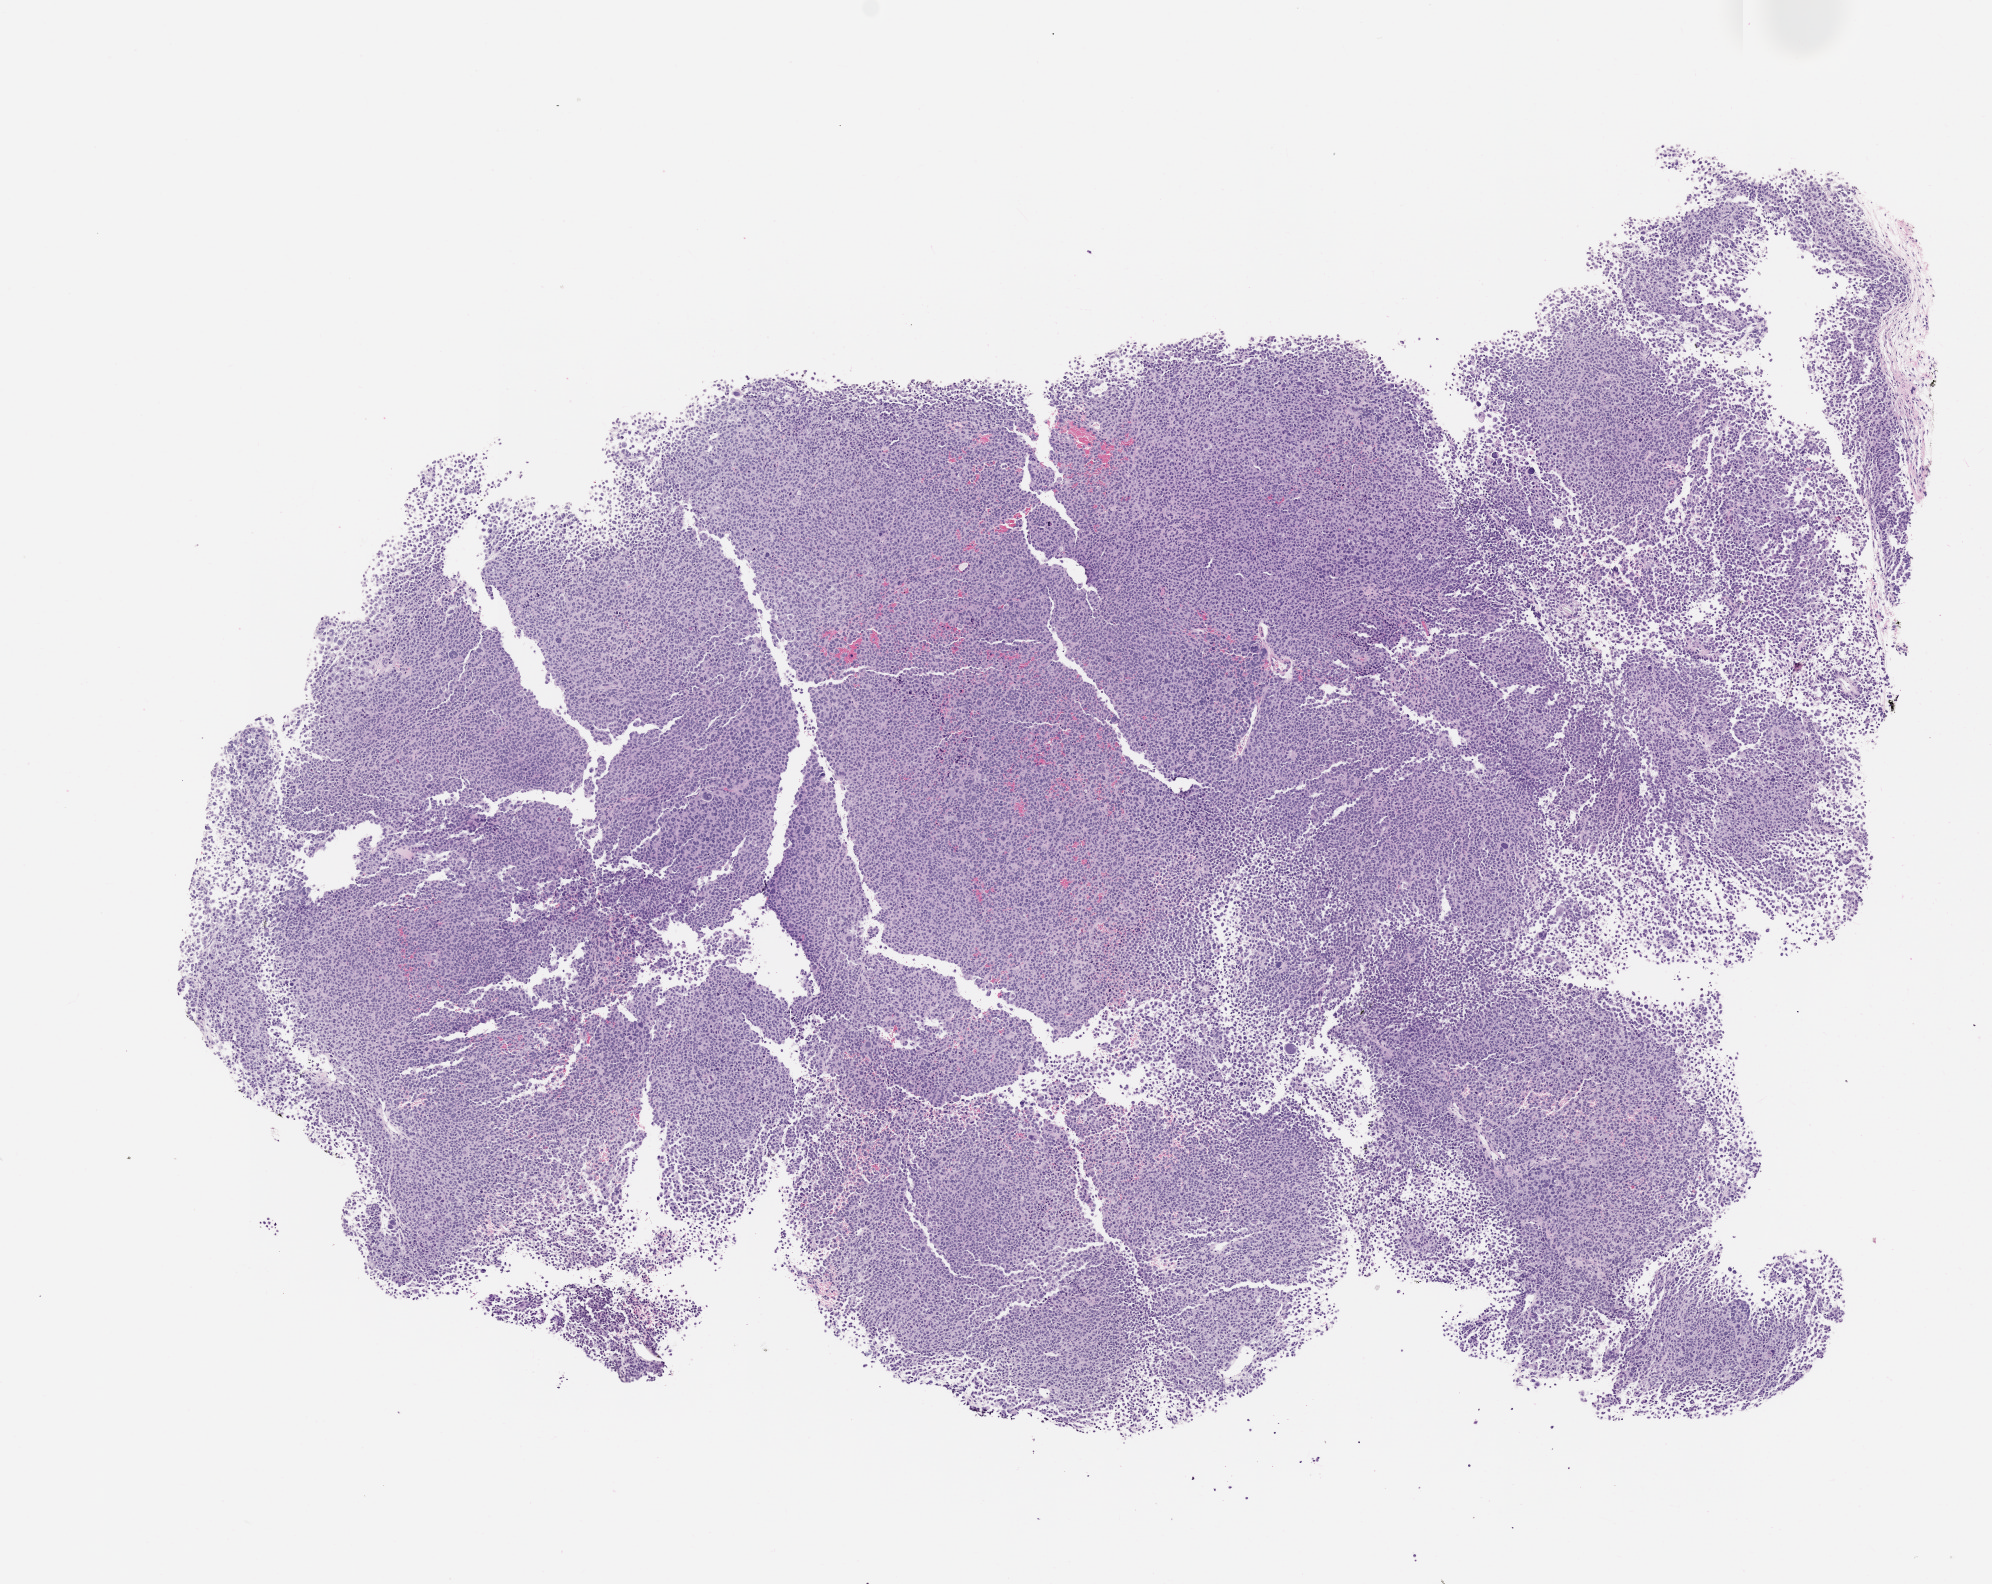
H&E whole-slide image of a patient-derived xenograft (PDX) tumor grown in a mouse, passage 1, a low-resolution overview of the entire scanned area, about 8.0 x 6.4 mm; FFPE section; originating tumor site category: skin.
Originating patient diagnosis: Melanoma.